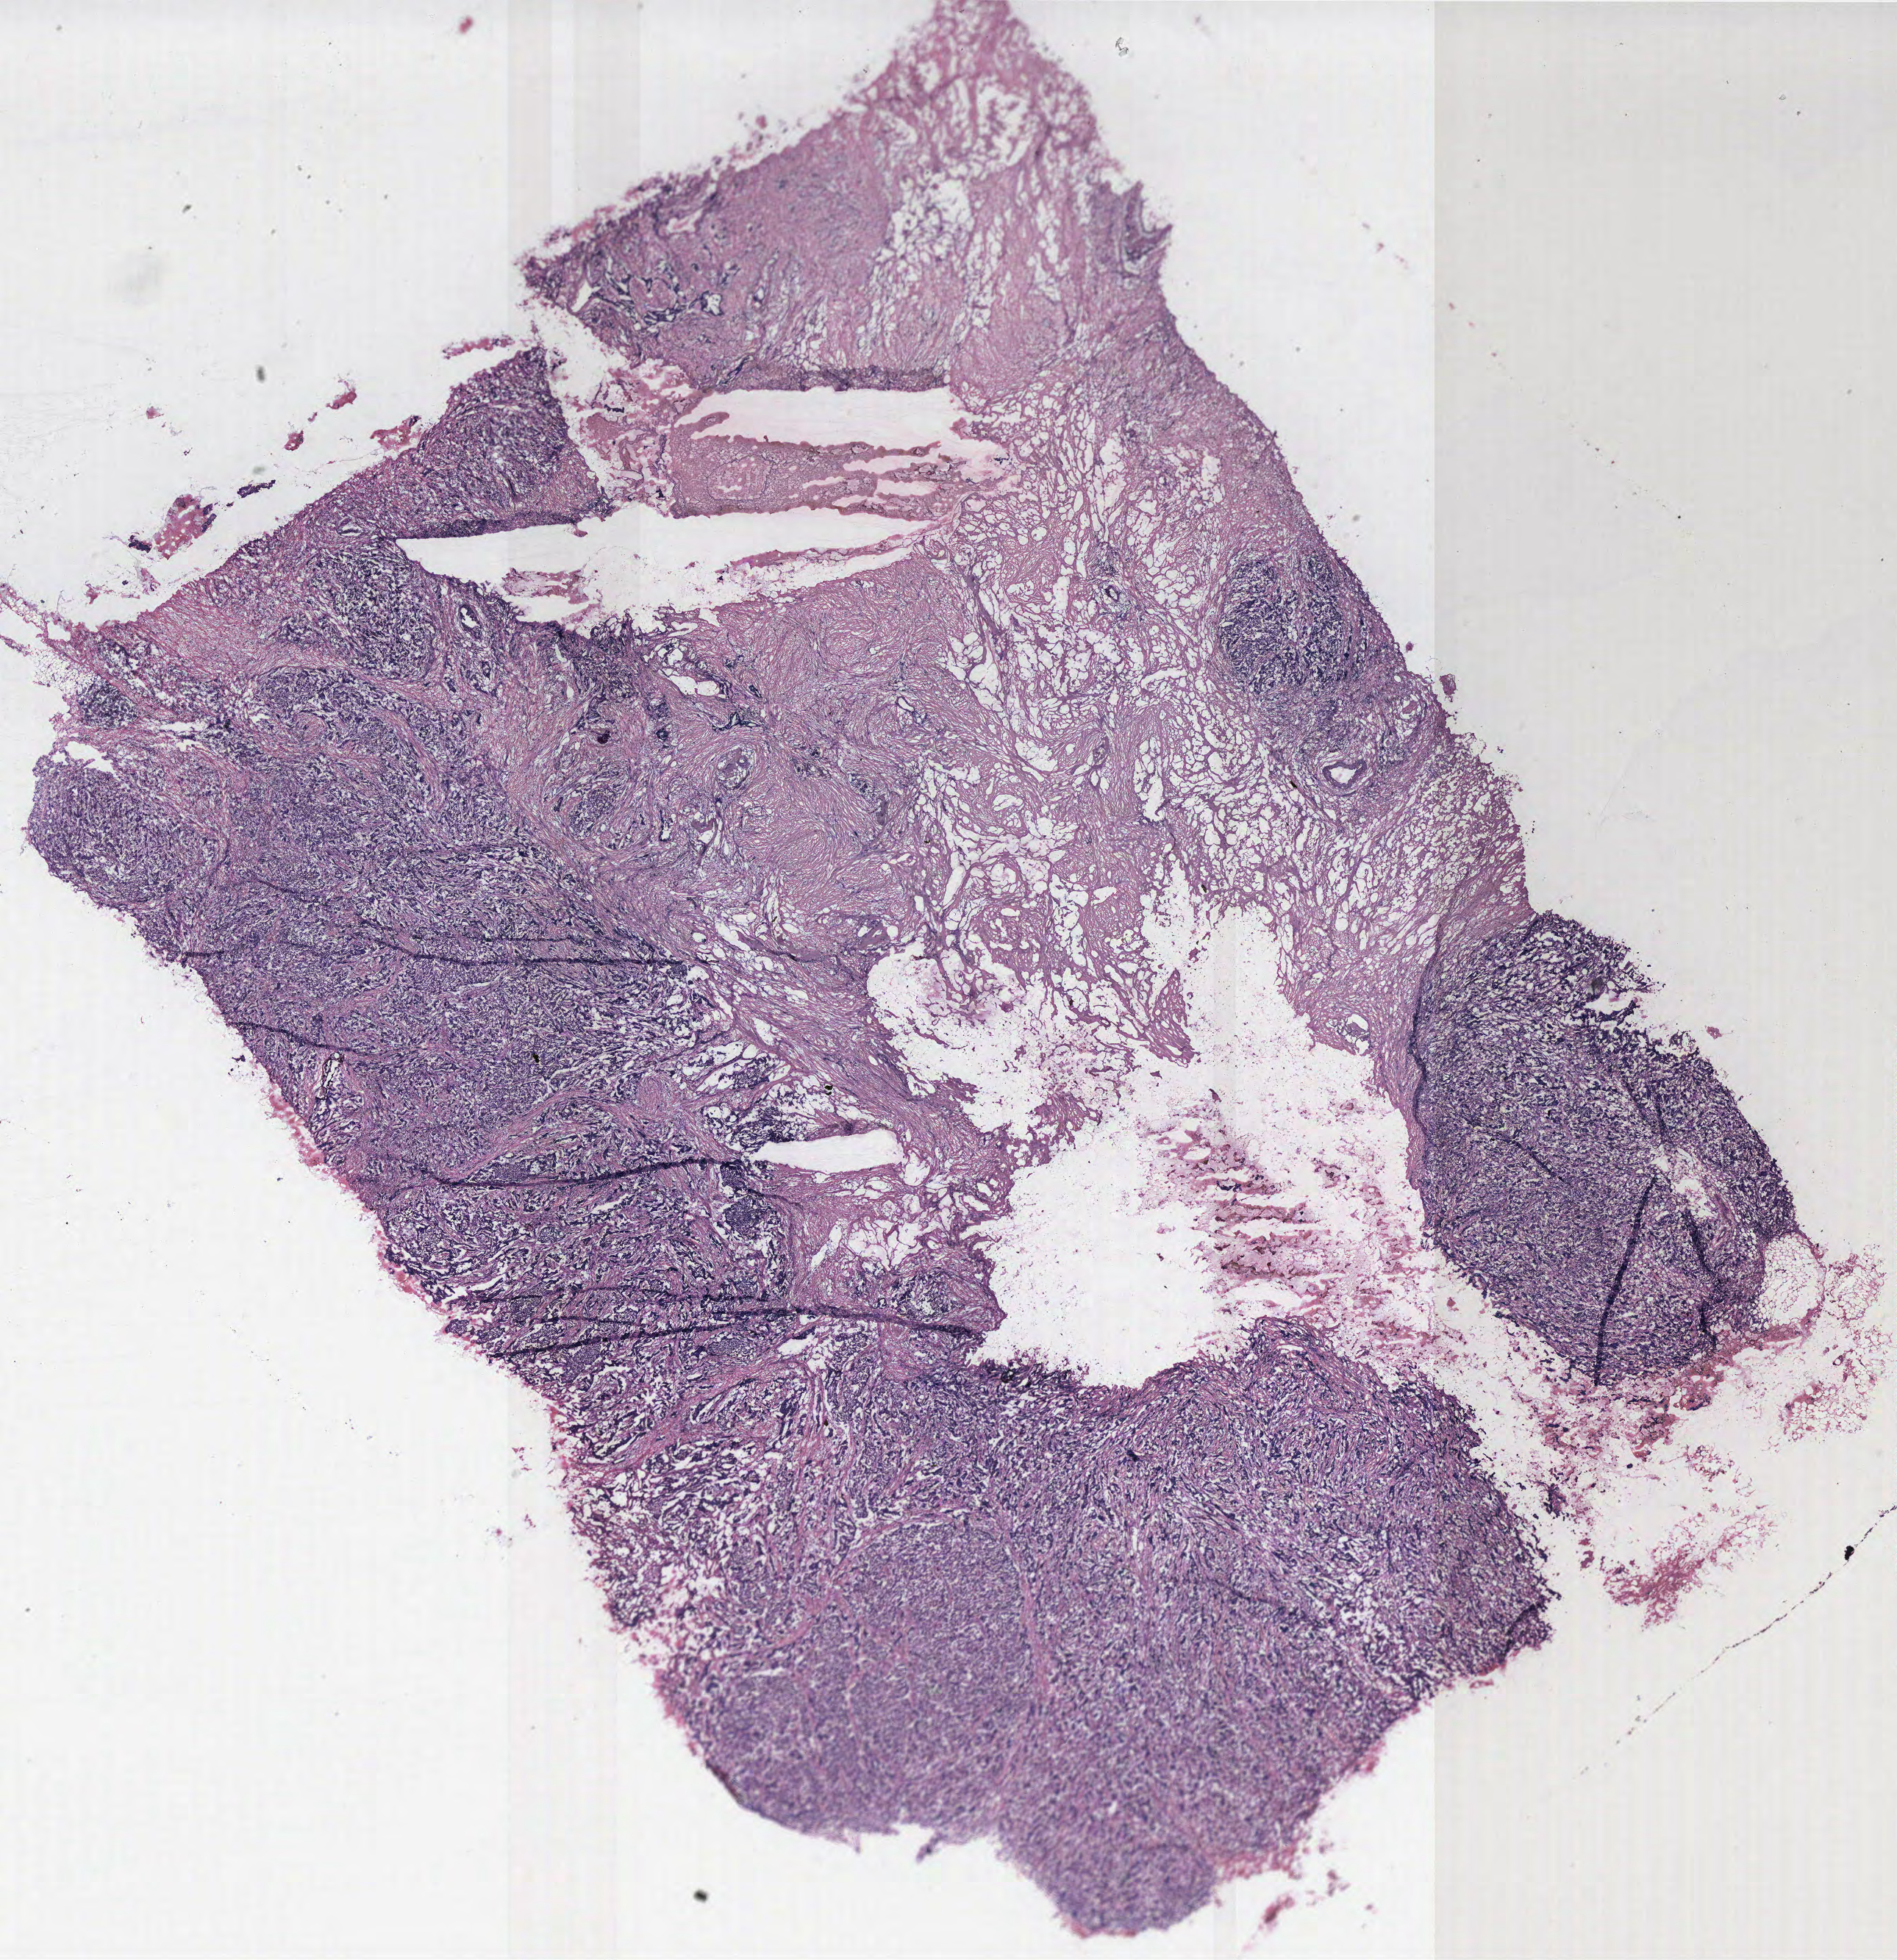
H&E-stained whole-slide image — shown as a low-resolution overview of the whole scanned area (about 20.6 x 21.3 mm, from a 40x scan), breast, tumour tissue. Female, 45 y/o.
• AJCC pathologic stage: IIIA
• histologic diagnosis: Infiltrating duct carcinoma, NOS